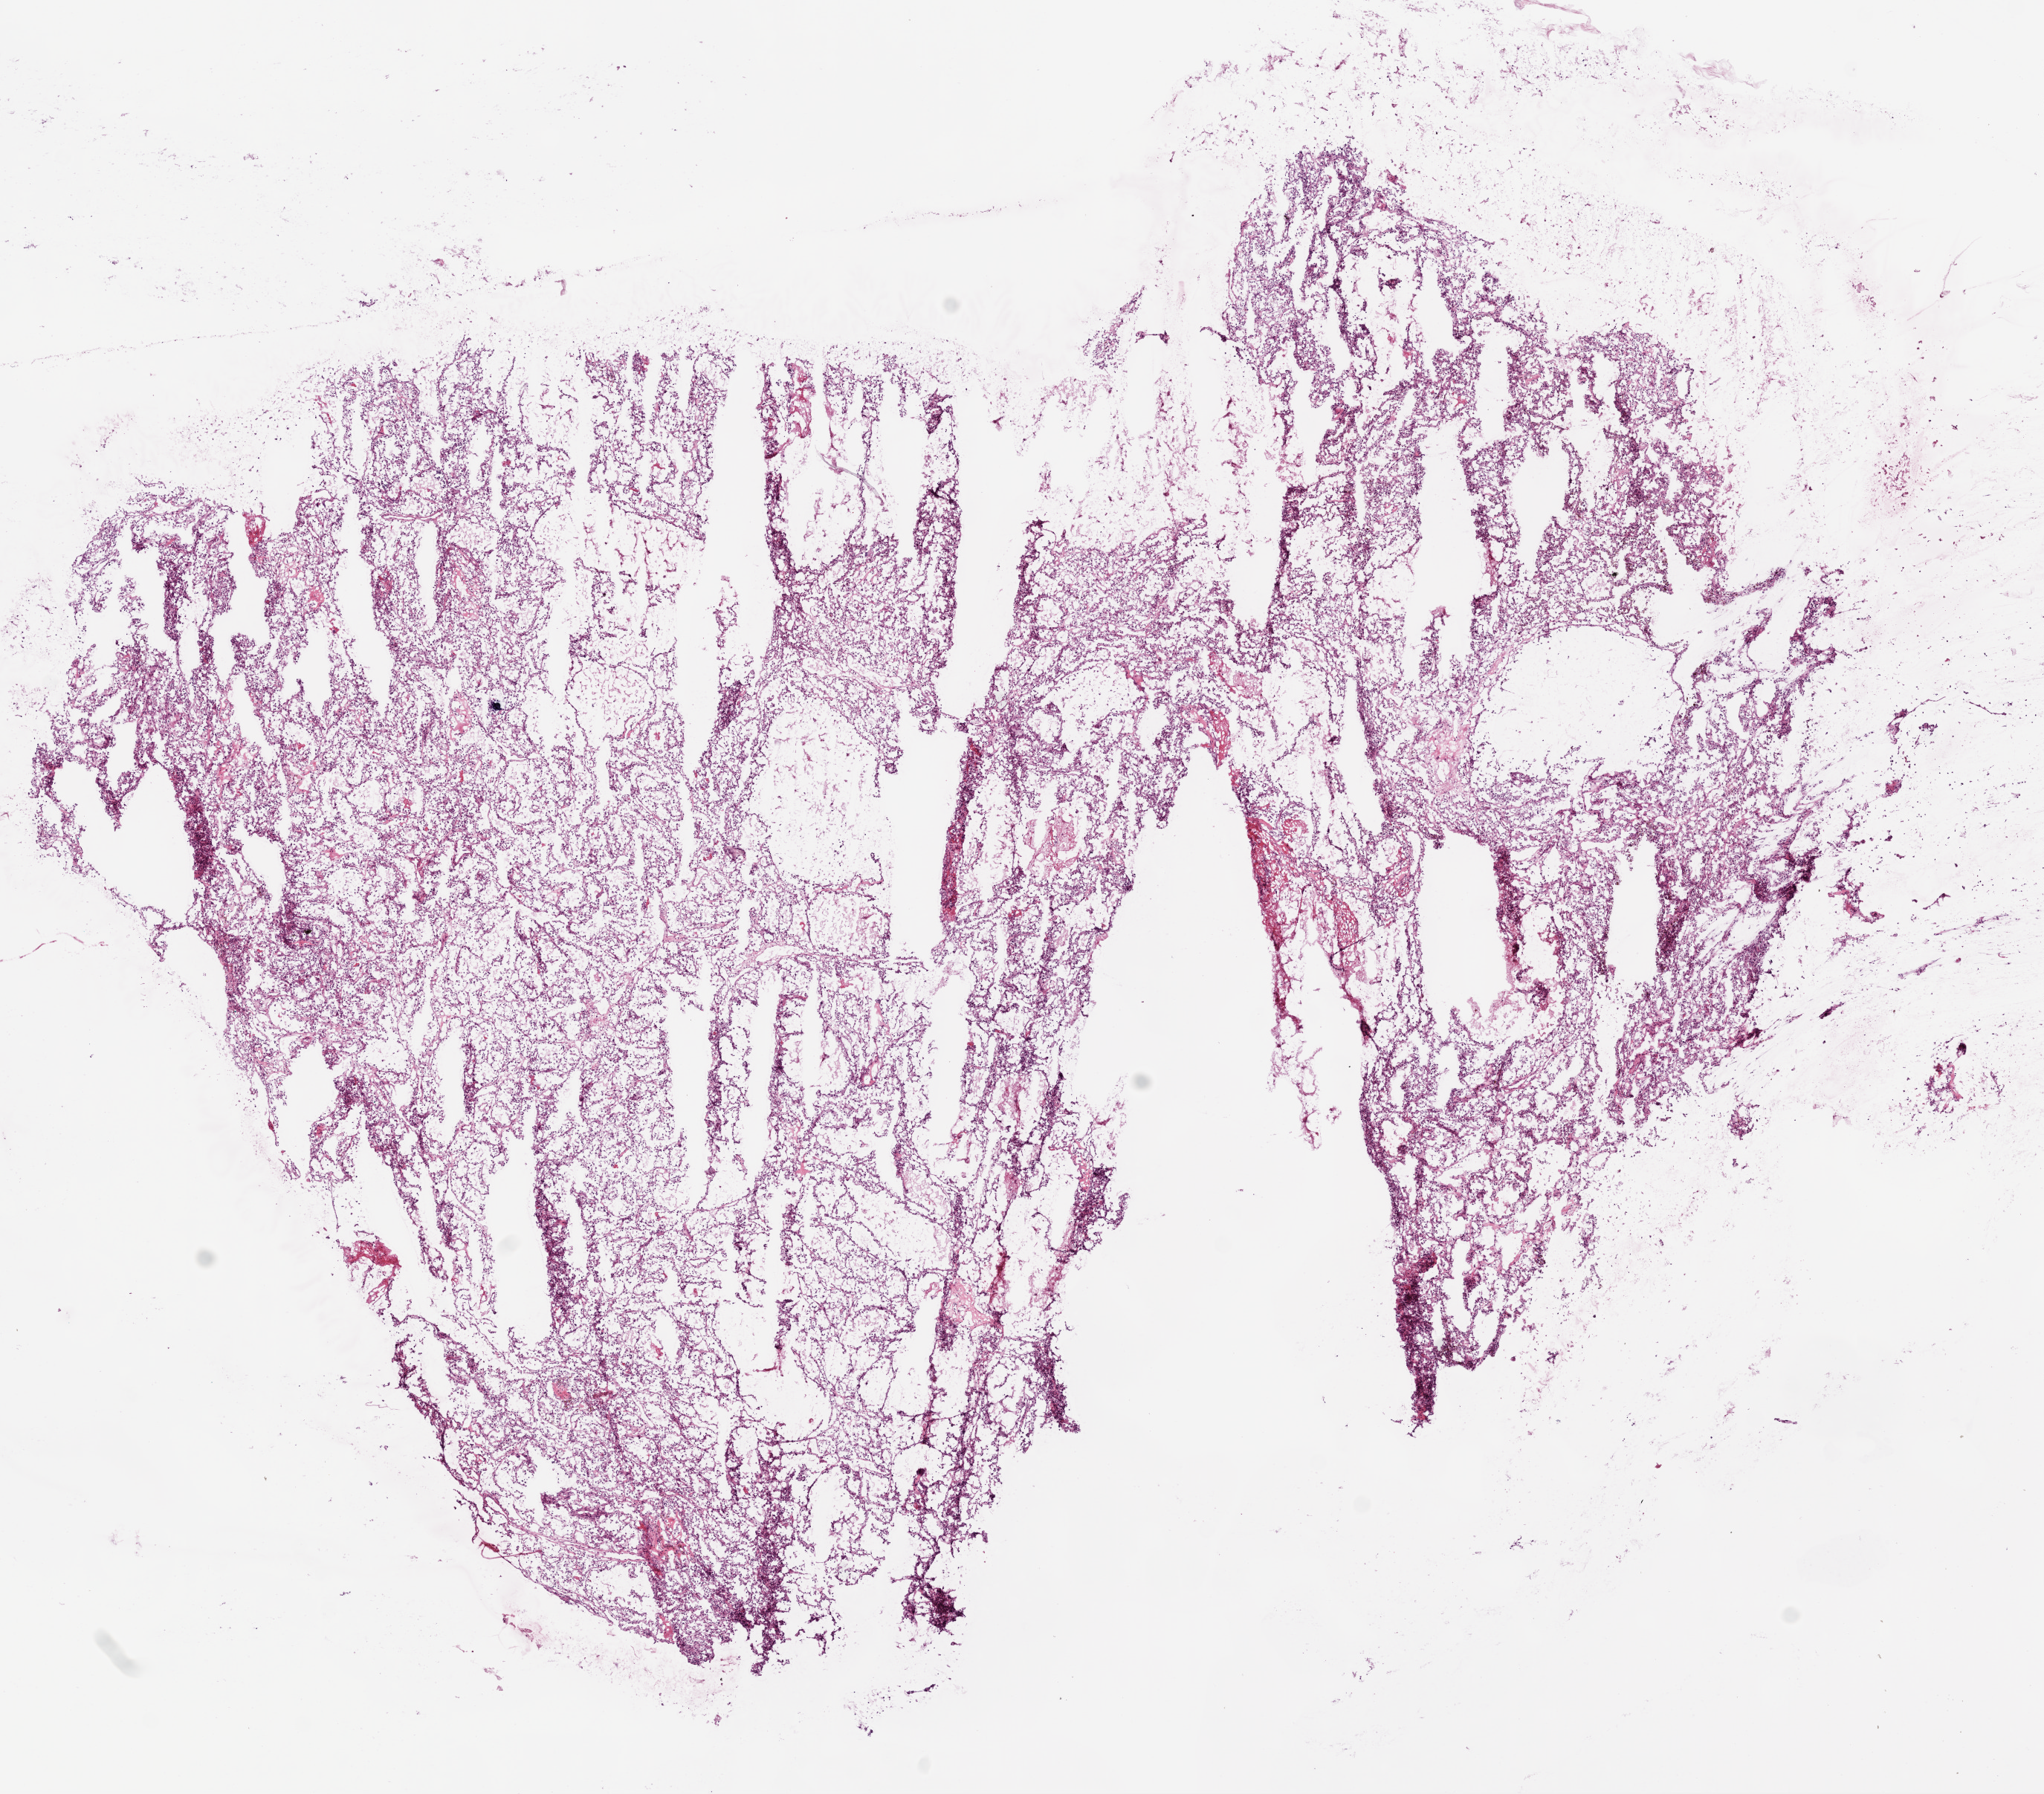
Digitized H&E tissue section (whole slide) — low-resolution overview of the scanned area, about 11.0 x 9.7 mm (from a 20x scan); frozen section from the top of the tissue portion; primary tumour sample from the kidney. Patient: male, age at initial diagnosis 77 years. Histologic grade: G3 (poorly differentiated). Composition of this section per pathologist review: tumour cells 90%, tumour nuclei 80%, normal cells 0%, stromal cells 10%, necrosis 0%.
Histologic diagnosis: Clear cell adenocarcinoma, NOS. Laterality: left. AJCC pathologic stage: I.